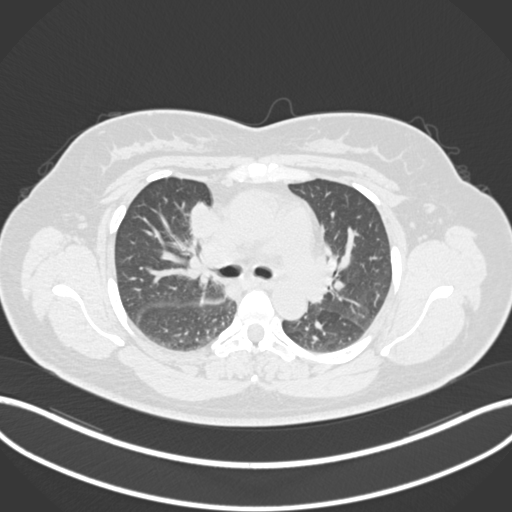
Chest CT, one axial slice. Slice 113 of 183 in the series (ordered by position). 120 kVp. Lung window (W 1500 / L -600 HU). 512 × 512 image matrix, field of view 400 × 400 mm. Female patient, age 46 years. From the clinical record (not read from this slice): clinical TNM (as recorded): T2a N1 M0.
Structures marked on this image (bounding box drawn by a radiologist):
- lung tumour (recorded histology: adenocarcinoma): bounding box (x1, y1, x2, y2) in pixels: (188, 198, 217, 239)